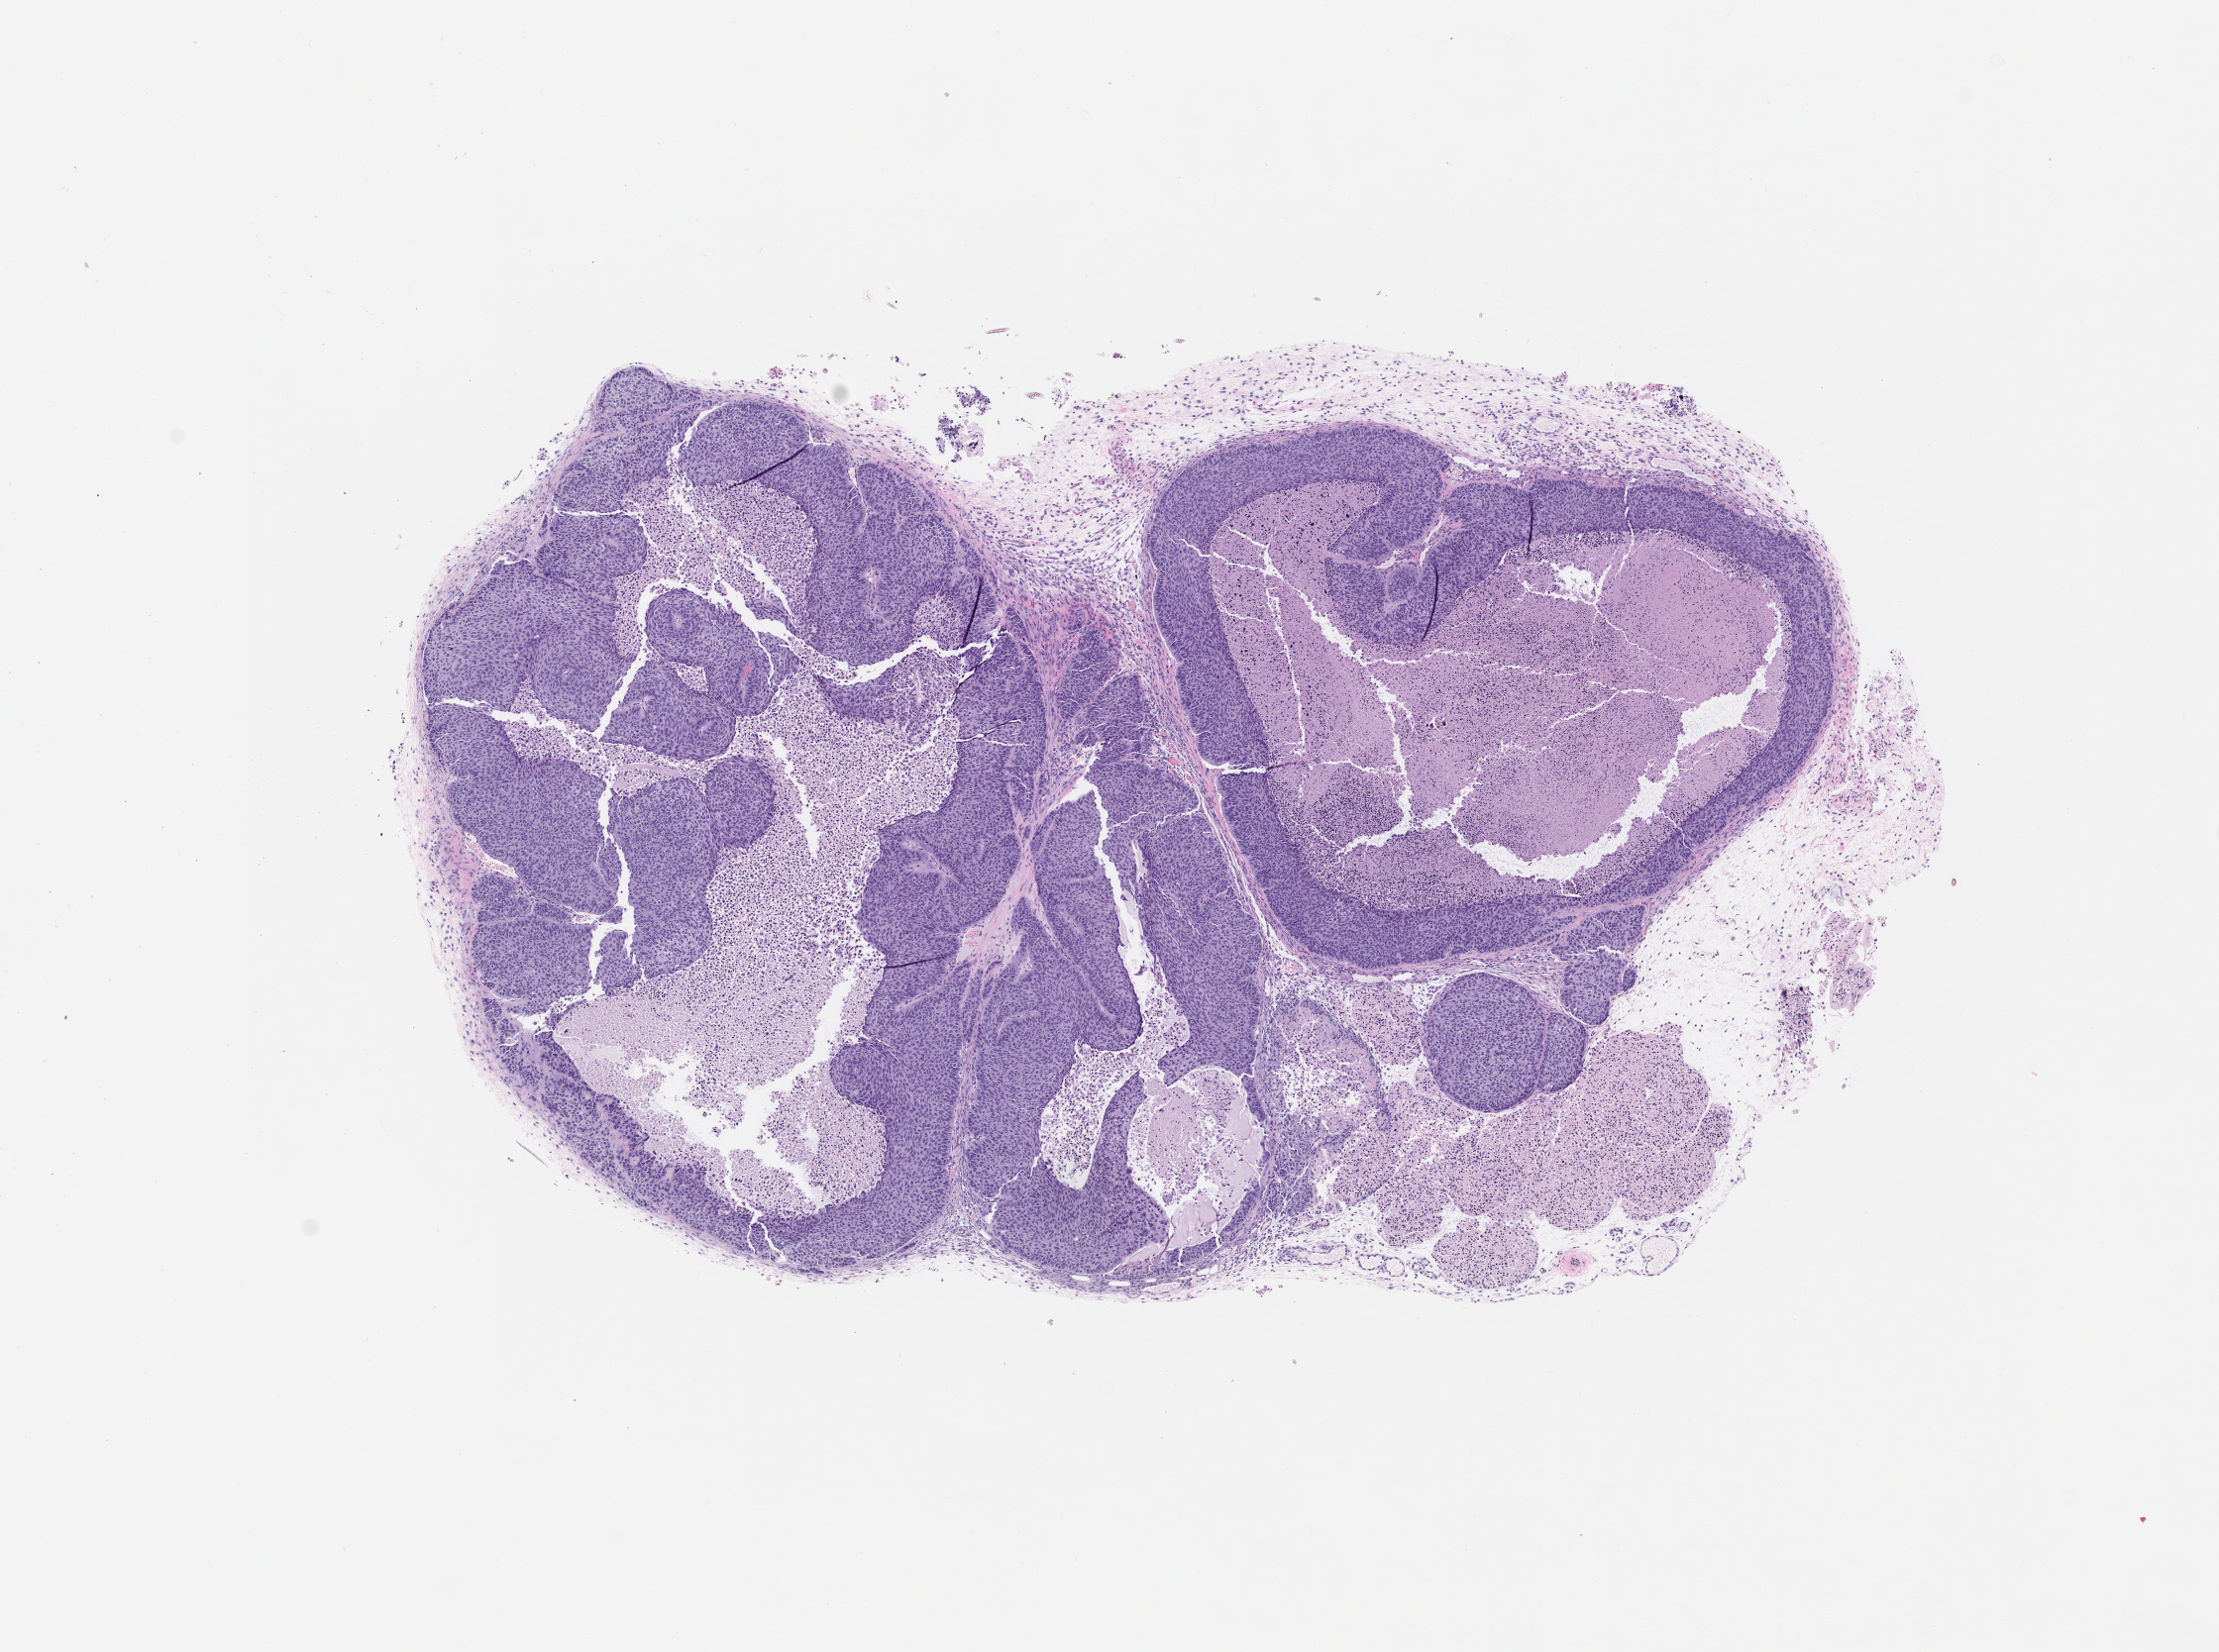
Whole-slide image, H&E: patient-derived xenograft (human tumor grown in a mouse), passage 1 — a low-resolution overview of the entire scanned area, about 9.0 x 6.7 mm, formalin-fixed paraffin-embedded section, originating tumor site category: lung.
Originating patient diagnosis: Lung Squamous Cell Carcinoma.